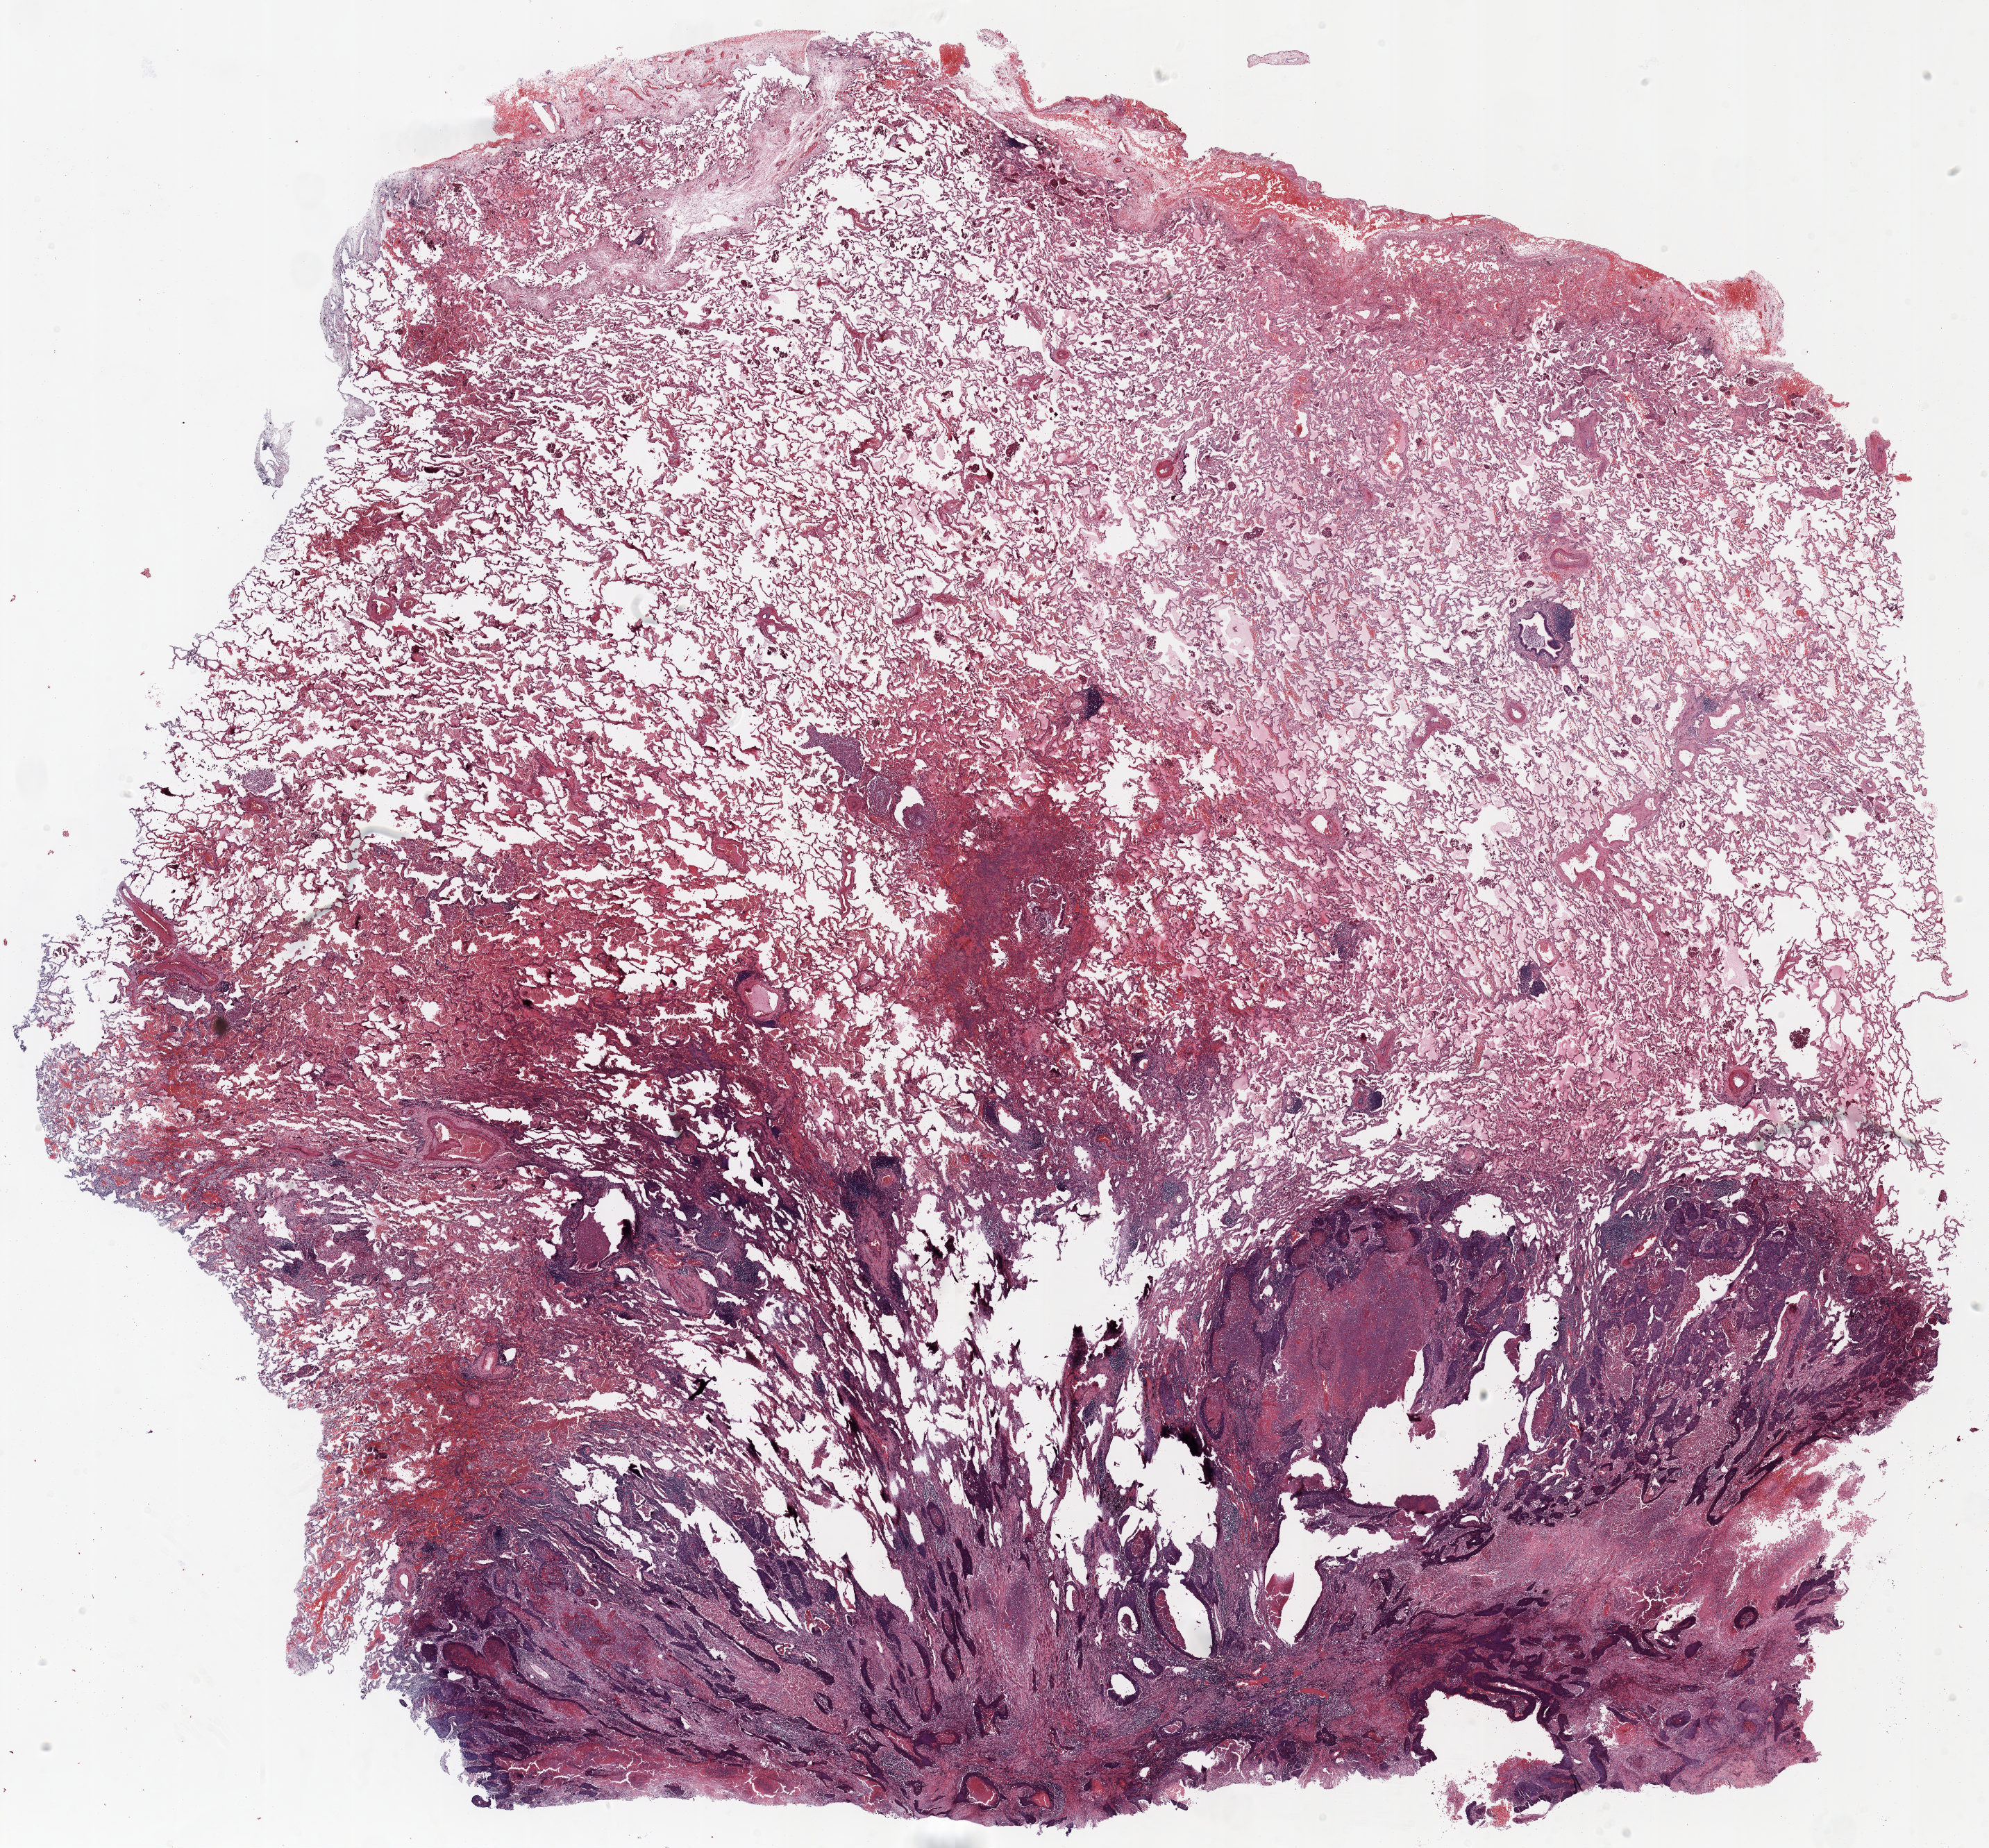
Whole-slide histology image, H&E-stained — low-resolution overview of the scanned area, about 23.0 x 21.4 mm (acquisition: 20x scan), FFPE section, lung tissue. Female, age 58 at enrolment. Current smoker at enrolment. Grade: poorly differentiated (G3).
Participant's lung-cancer diagnosis: Non-small cell carcinoma (ICD-O-3 8046/3). Tumour size (pathology): 25 mm. Stage (AJCC 6th edition): IA. Primary tumour location (clinical record): right lower lobe.